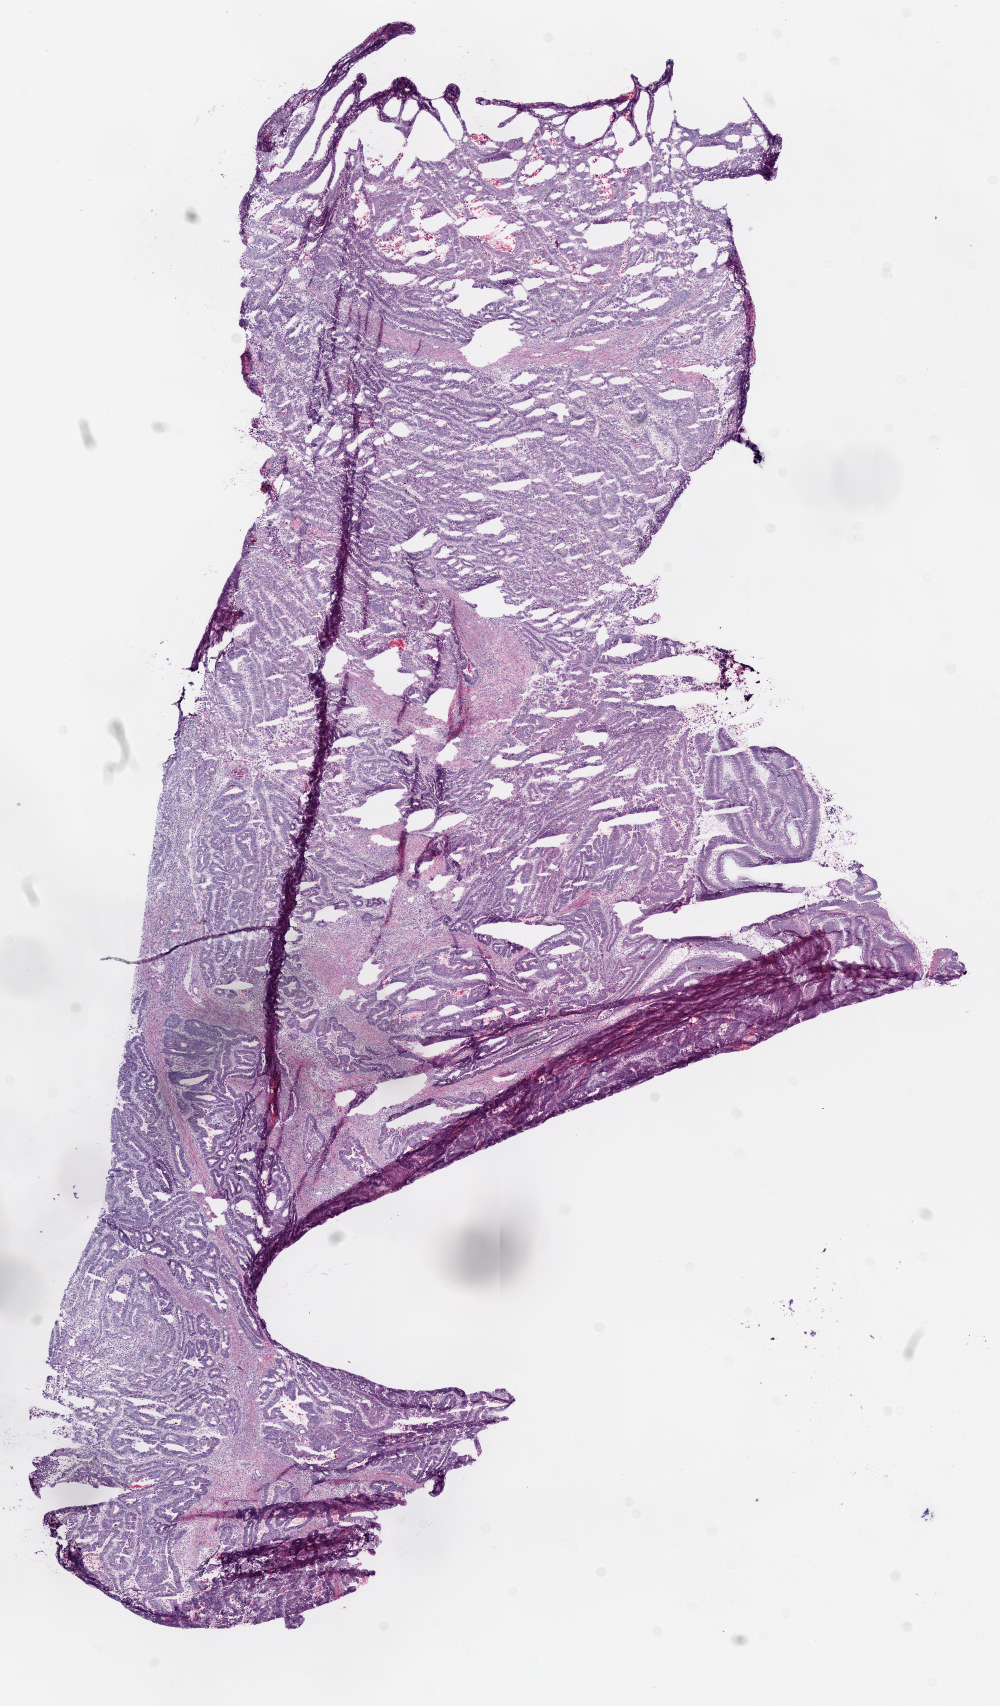
Digitized H&E-stained tissue section (whole slide), shown as a low-resolution overview of the whole scanned area (about 8.0 x 13.7 mm). Frozen section from the bottom of the tissue portion. Sample: primary tumour, rectum. Female patient; age at initial diagnosis 48 years. Pathologist review of this section (percent, as recorded): tumour cells 87%, tumour nuclei 80%, normal cells 0%, stromal cells 10%, necrosis 3%.
• diagnosis: Adenocarcinoma, NOS (rectosigmoid junction)
• AJCC pathologic stage: I